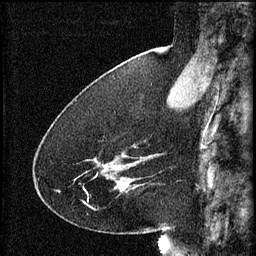
Breast MRI (dynamic contrast-enhanced), one sagittal slice. Position 23 of 60 along the scan axis. 3 images stored at this slice position (order not interpretable as contrast timing). 1.5 T. TE 4.2 ms, TR 8.2 ms. 2 mm slice thickness. 256 × 256 image matrix, field of view 180 × 180 mm. Patient: female, 41 years.
Annotated regions visible in this slice (semi-automatically segmented with operator editing):
- analysis volume of interest (the breast-tissue region the enhancement analysis was run in; not a lesion): bounding box <77,154,134,195> (left, top, right, bottom; pixels)
- tumour enhancement mask (voxels above the 70 % enhancement threshold inside the analysis volume of interest): <97,156,133,191>